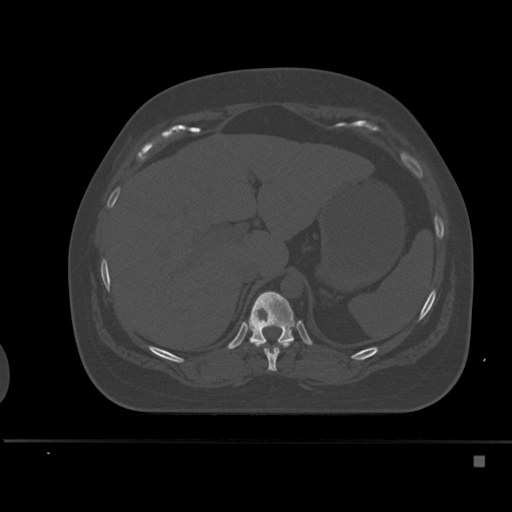
CT including the spine, one axial slice. Position 238 of 495 along the scan axis. Bone window (W 1800 / L 400 HU). 512 × 512 image matrix. Patient: female, 33 years. Case-level facts recorded for this patient, not image findings: primary cancer: breast.
Outlined on this slice (semi-automatic segmentation, software-assisted and operator-edited):
- T10 vertebra: bounding box <252,341,291,371> (left, top, right, bottom; pixels)
- T11 vertebra: <244,291,298,345>